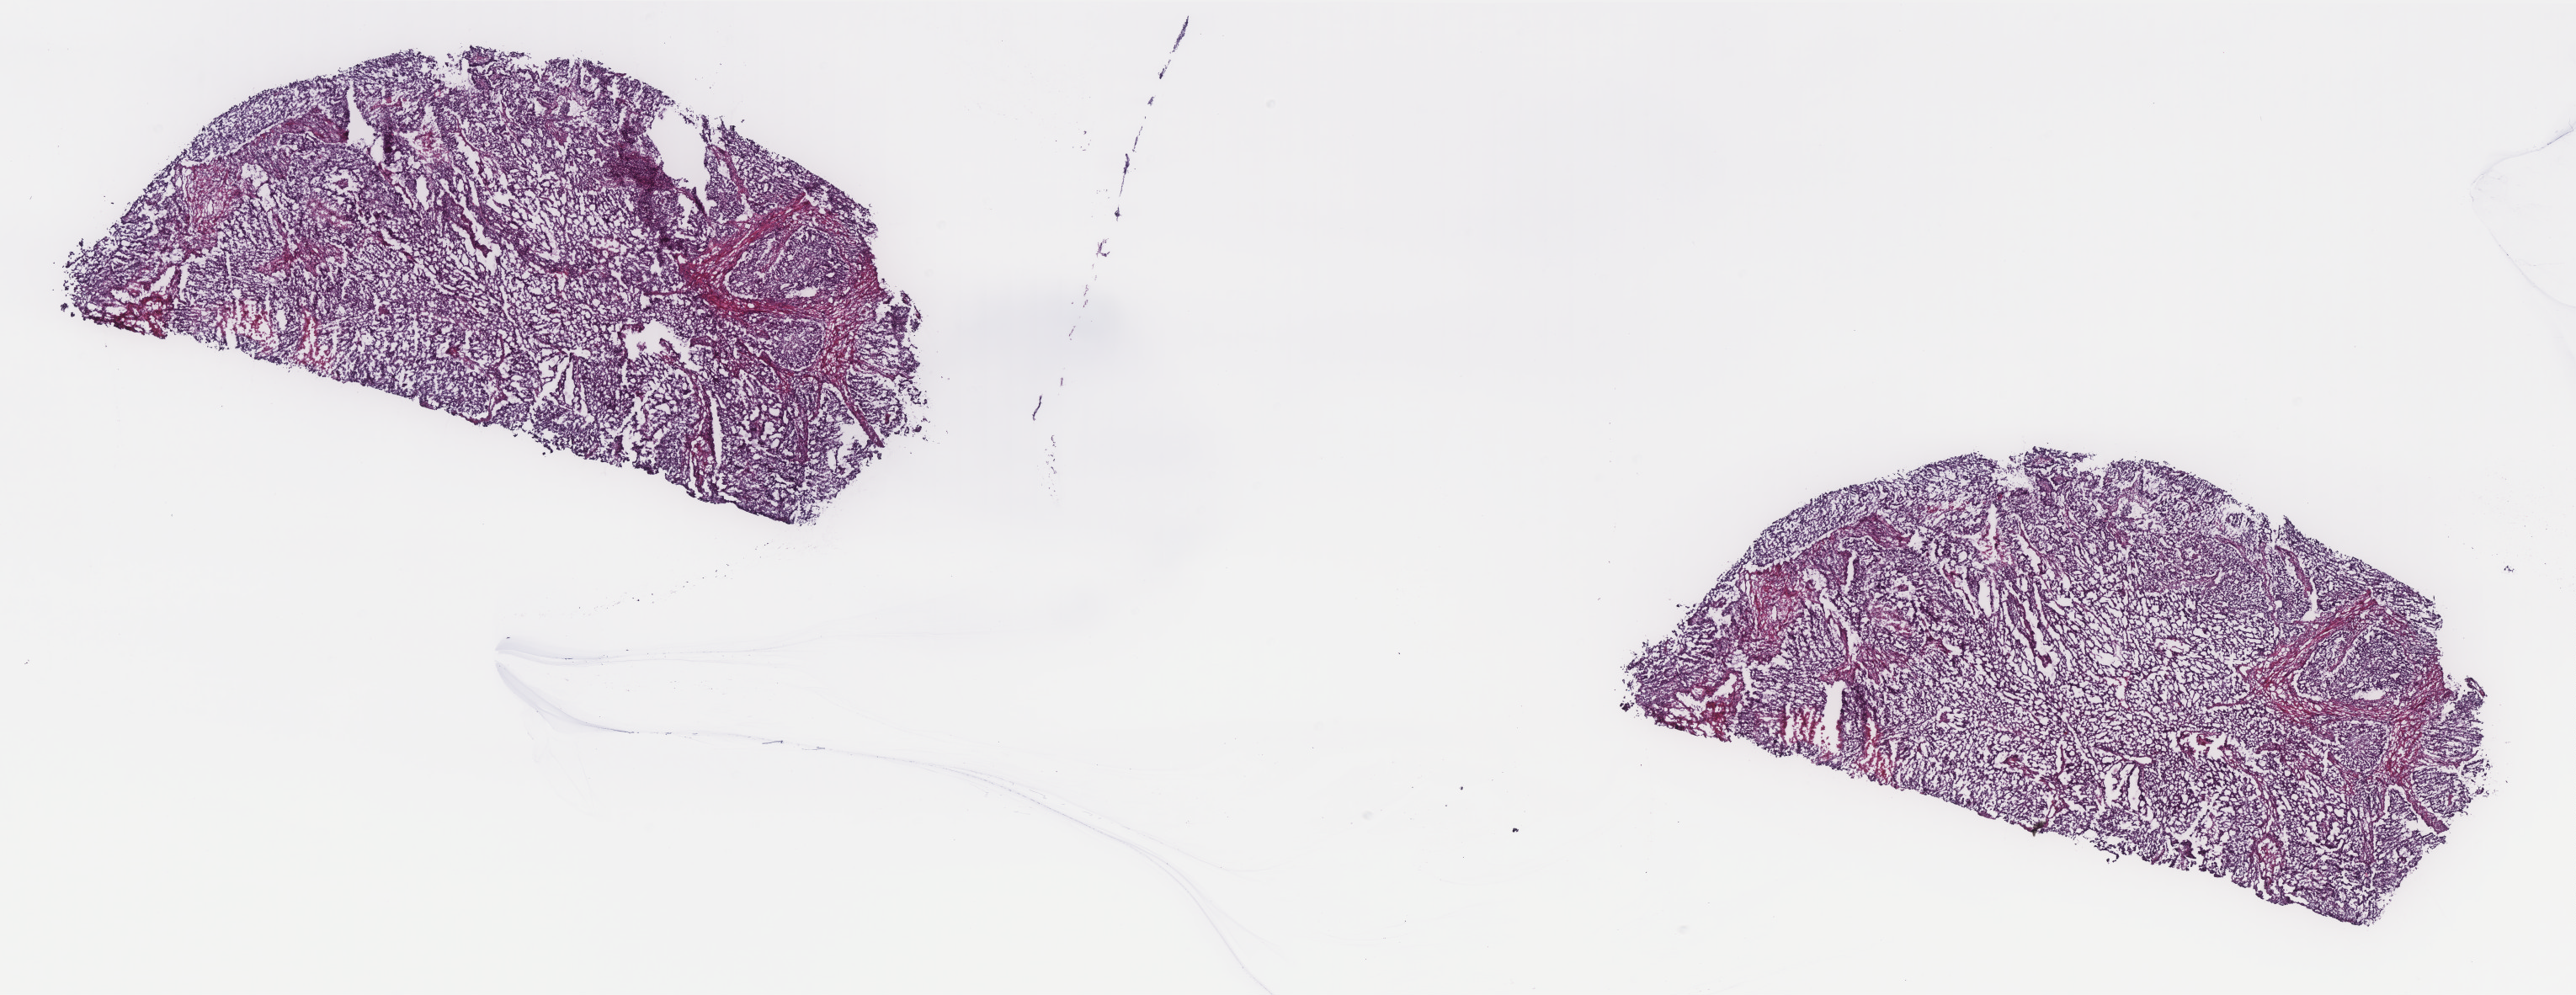
Digitized H&E-stained tissue section (whole slide) — shown as a low-resolution overview of the whole scanned area (about 24.5 x 9.5 mm), frozen section from the top of the tissue portion, uterus, primary tumour sample. Patient: female, age at initial diagnosis 40 years. Histologic grade: G2 (moderately differentiated). Pathologist review of this section (percent, as recorded): tumour cells 100%, tumour nuclei 85%, normal cells 0%, stromal cells 0%, necrosis 0%. Inflammatory infiltration, as recorded: lymphocyte infiltration 0%, monocyte infiltration 0%, neutrophil infiltration 0%.
FIGO stage: IIIC2. Pathologic diagnosis: Endometrioid adenocarcinoma, NOS. Lymph nodes positive (case pathology): 0 of 3 examined.